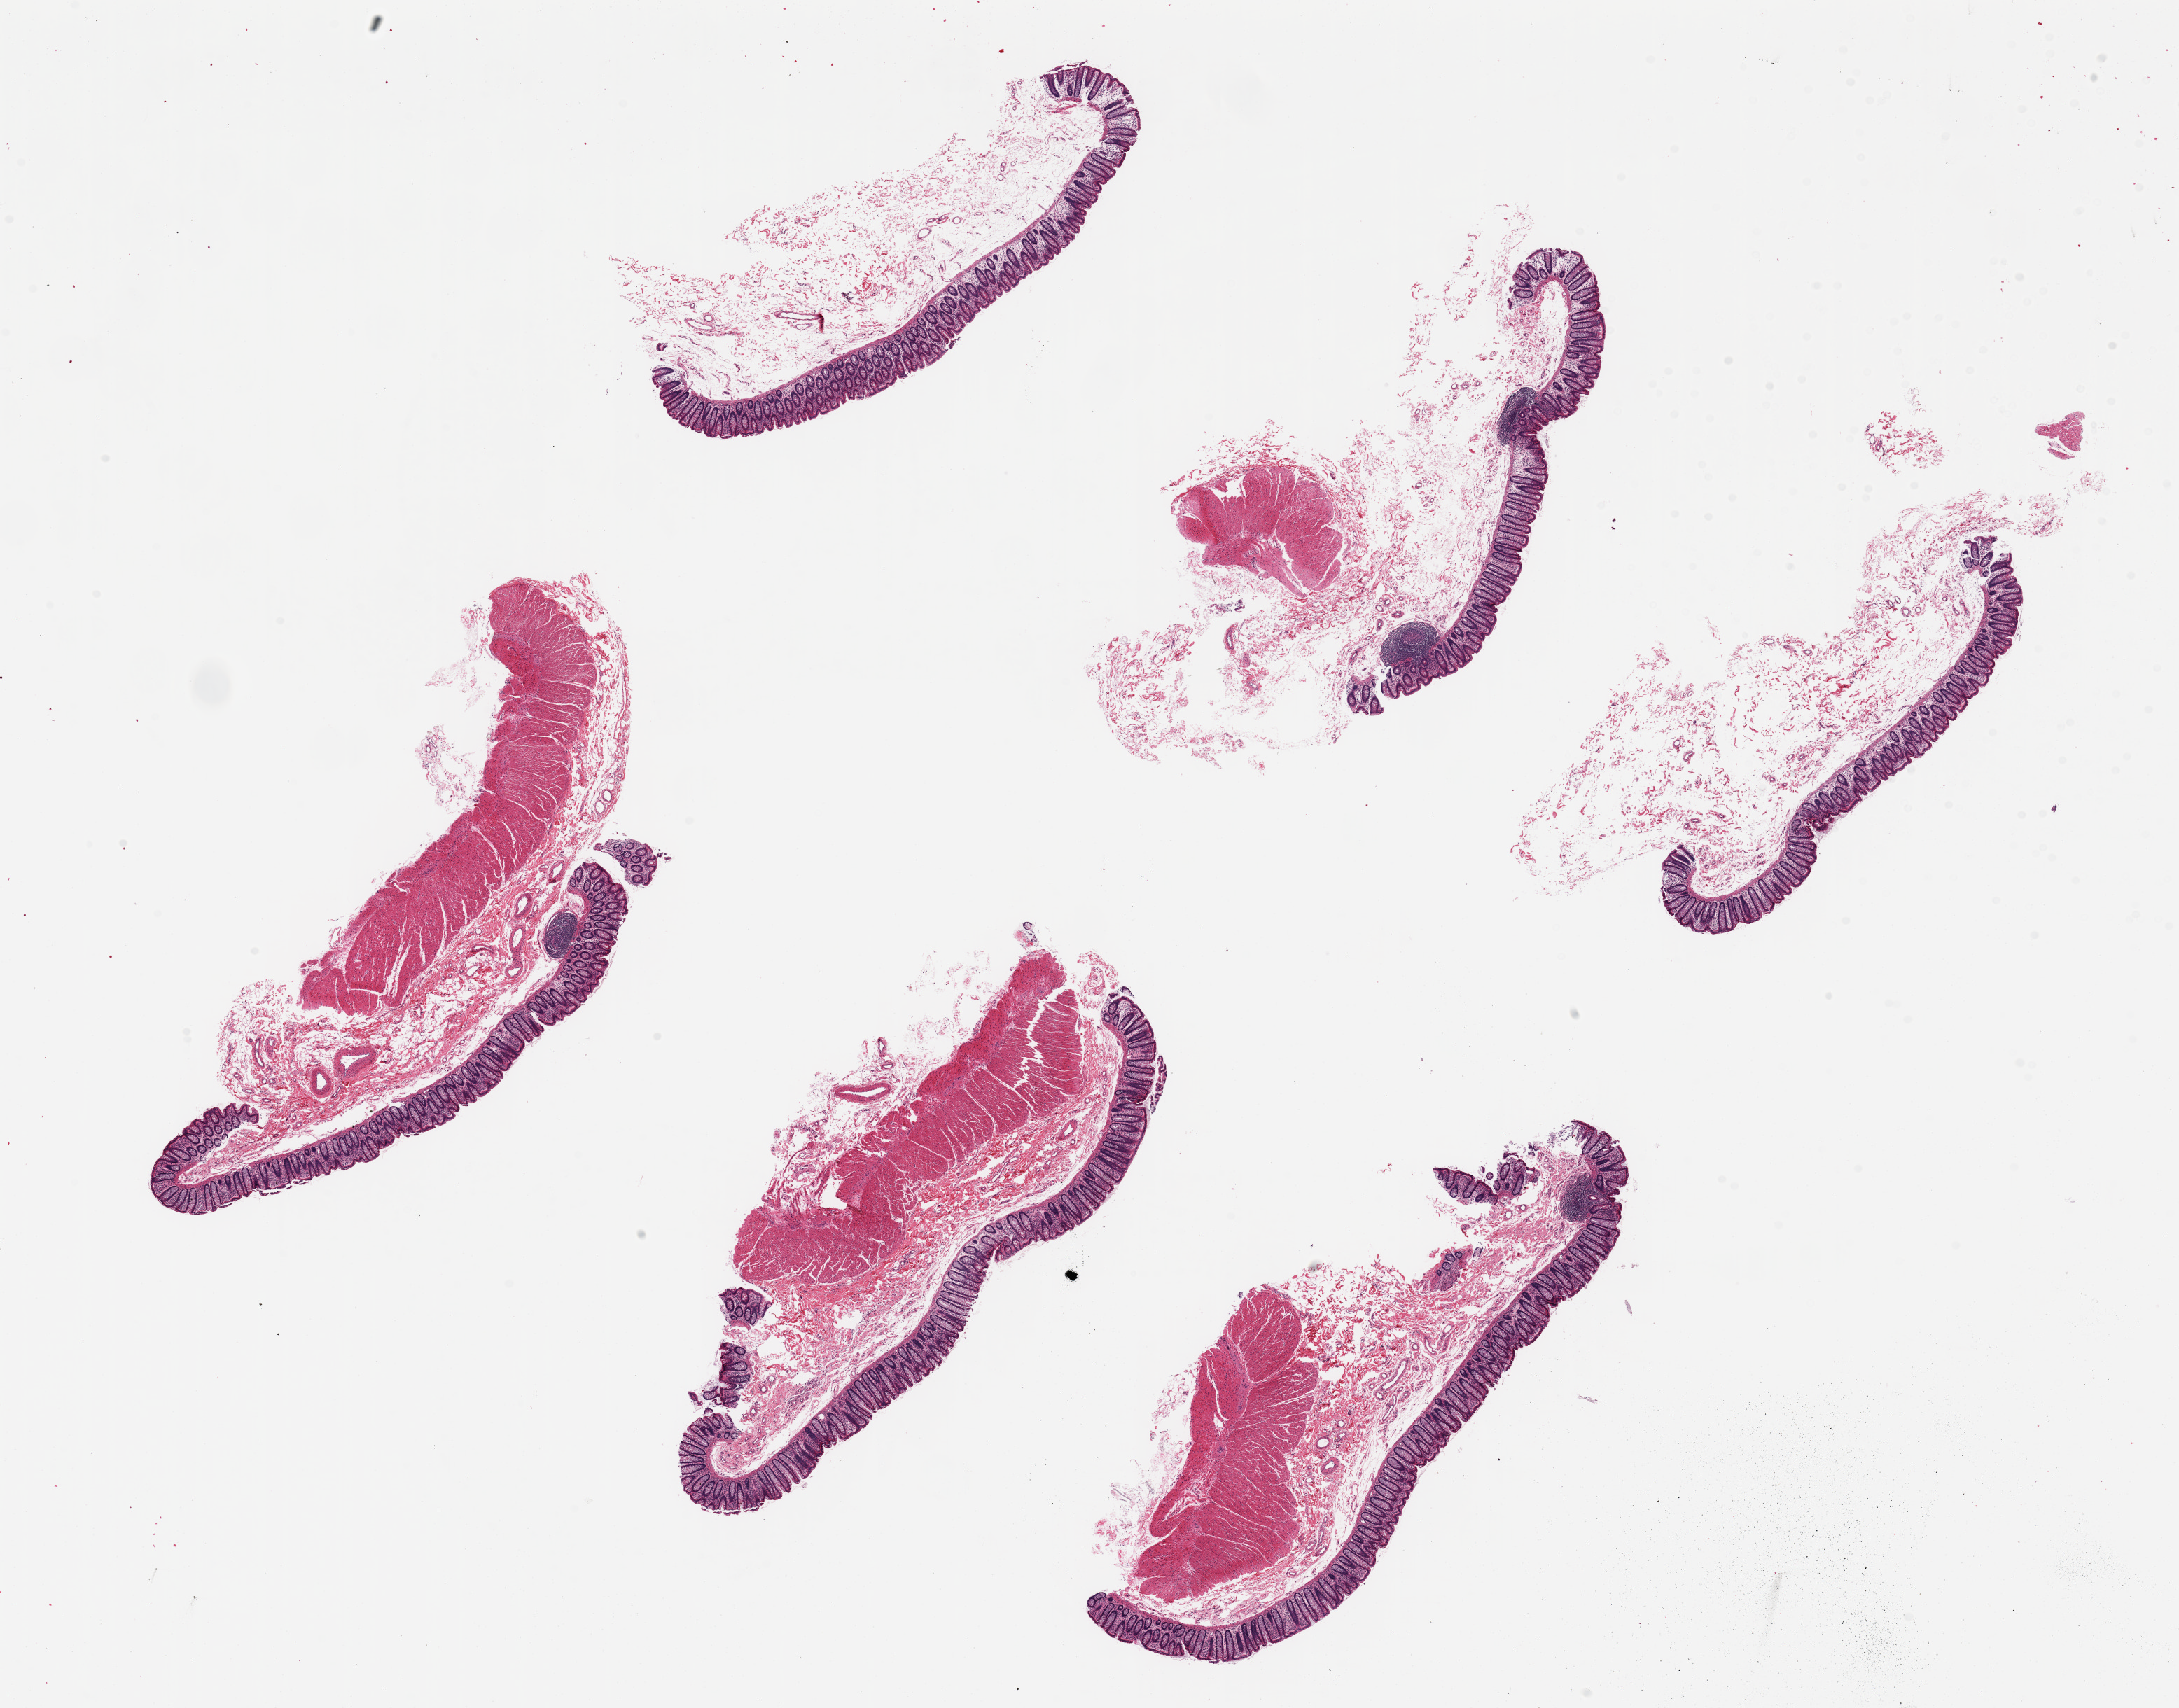
Digitized H&E-stained section — low-resolution overview of the scanned area, about 24.6 x 19.3 mm; PAXgene-fixed paraffin-embedded (PFPE) section; sampled site (target tissue): transverse colon; tissue donor sample.
* review note (as recorded): 6 pieces up to 8x3 mm; ~540um thick mucosa; muscularis propria on 4 pieces